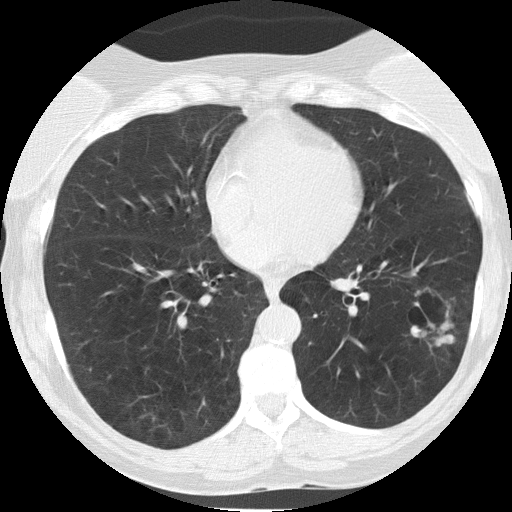
Axial slice from a low-dose chest CT screening exam. First (baseline) screen. Lung window (W 1500 / L -600 HU). Slice 85 of 149 in the series. 512 × 512 image matrix. Female participant, aged 58 years at enrolment. Current smoker at enrolment.
Expert reader's lesion annotation, bounding box <405,306,459,348> (left, top, right, bottom; pixels). The screening reader recorded 3 non-calcified nodules or masses ≥4 mm on this exam (right lower lobe, lingula, left lower lobe); which of them this box marks is not recorded.